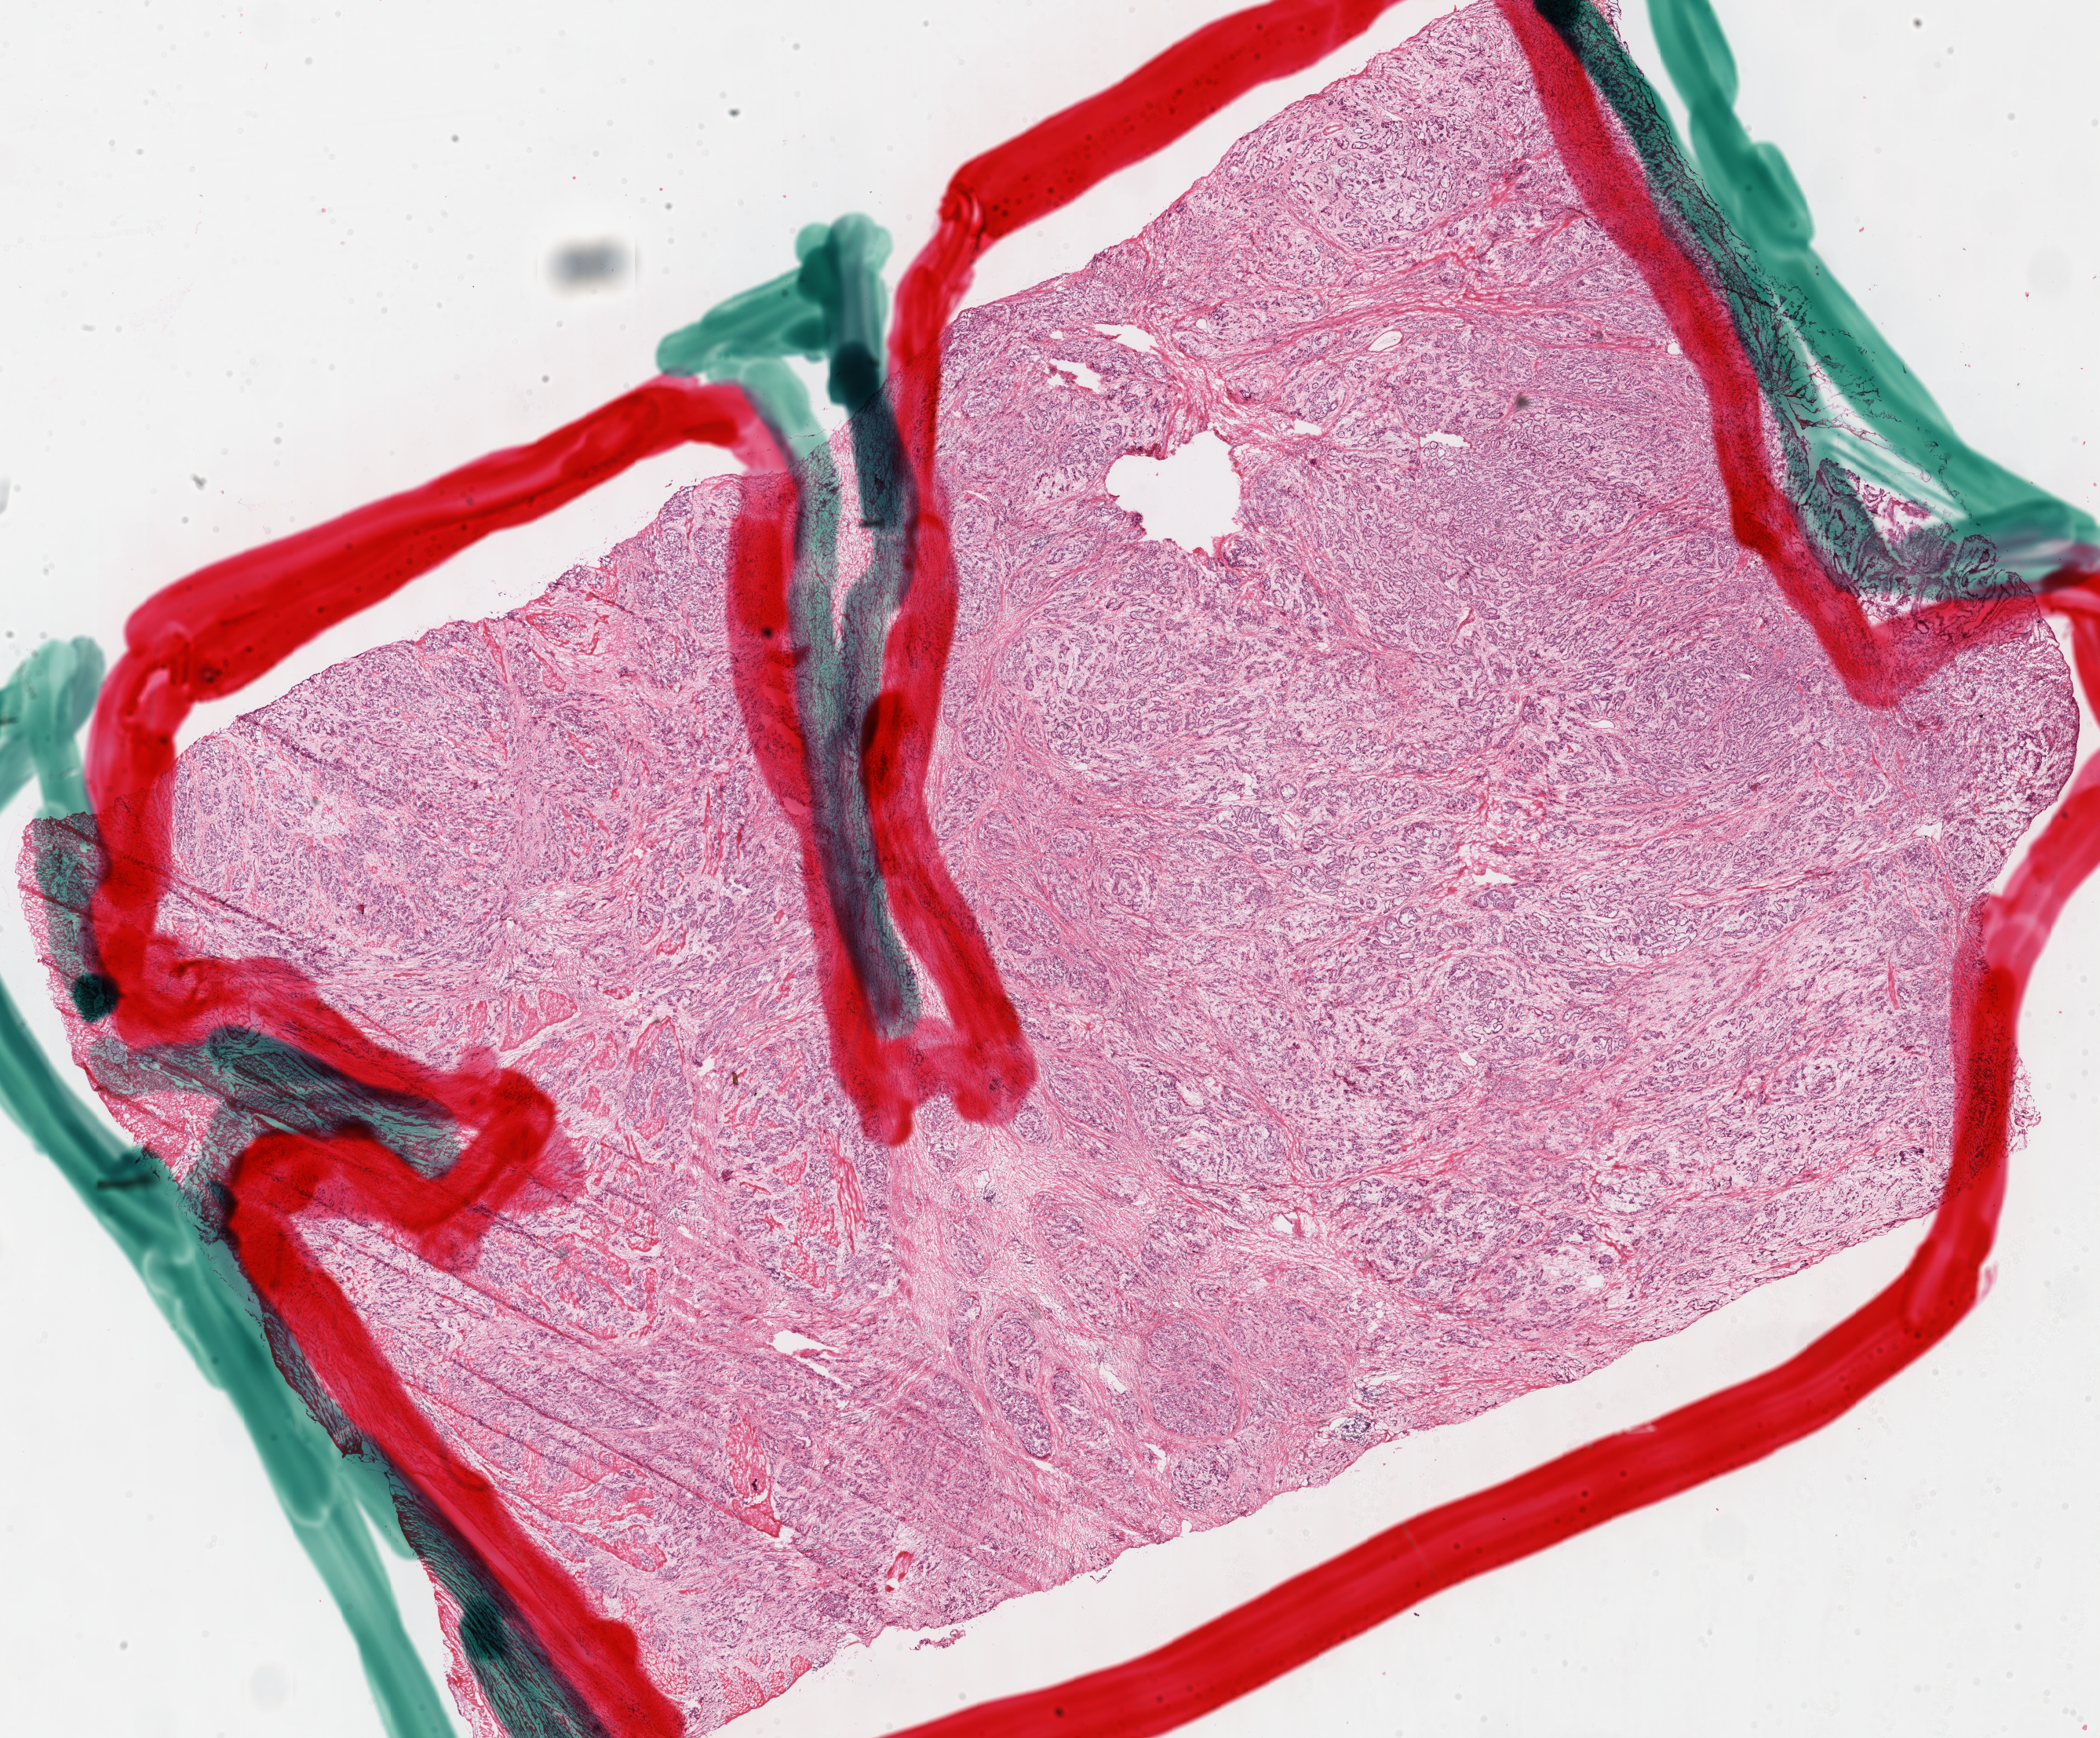
Whole-slide histology image, Hematoxylin and eosin (H&E) stained, whole scanned area (about 21.0 x 17.4 mm) shown as a low-resolution overview. Frozen section from the top of the tissue portion. Primary tumour sample from the stomach. Patient: male, age at initial diagnosis 57 years. Histologic grade: G3 (poorly differentiated). Composition of this section per pathologist review: tumour cells 85%, tumour nuclei 85%, normal cells 0%, stromal cells 15%, necrosis 0%.
AJCC pathologic stage: IV (7th edition). Histologic diagnosis: Adenocarcinoma, intestinal type (body of stomach).